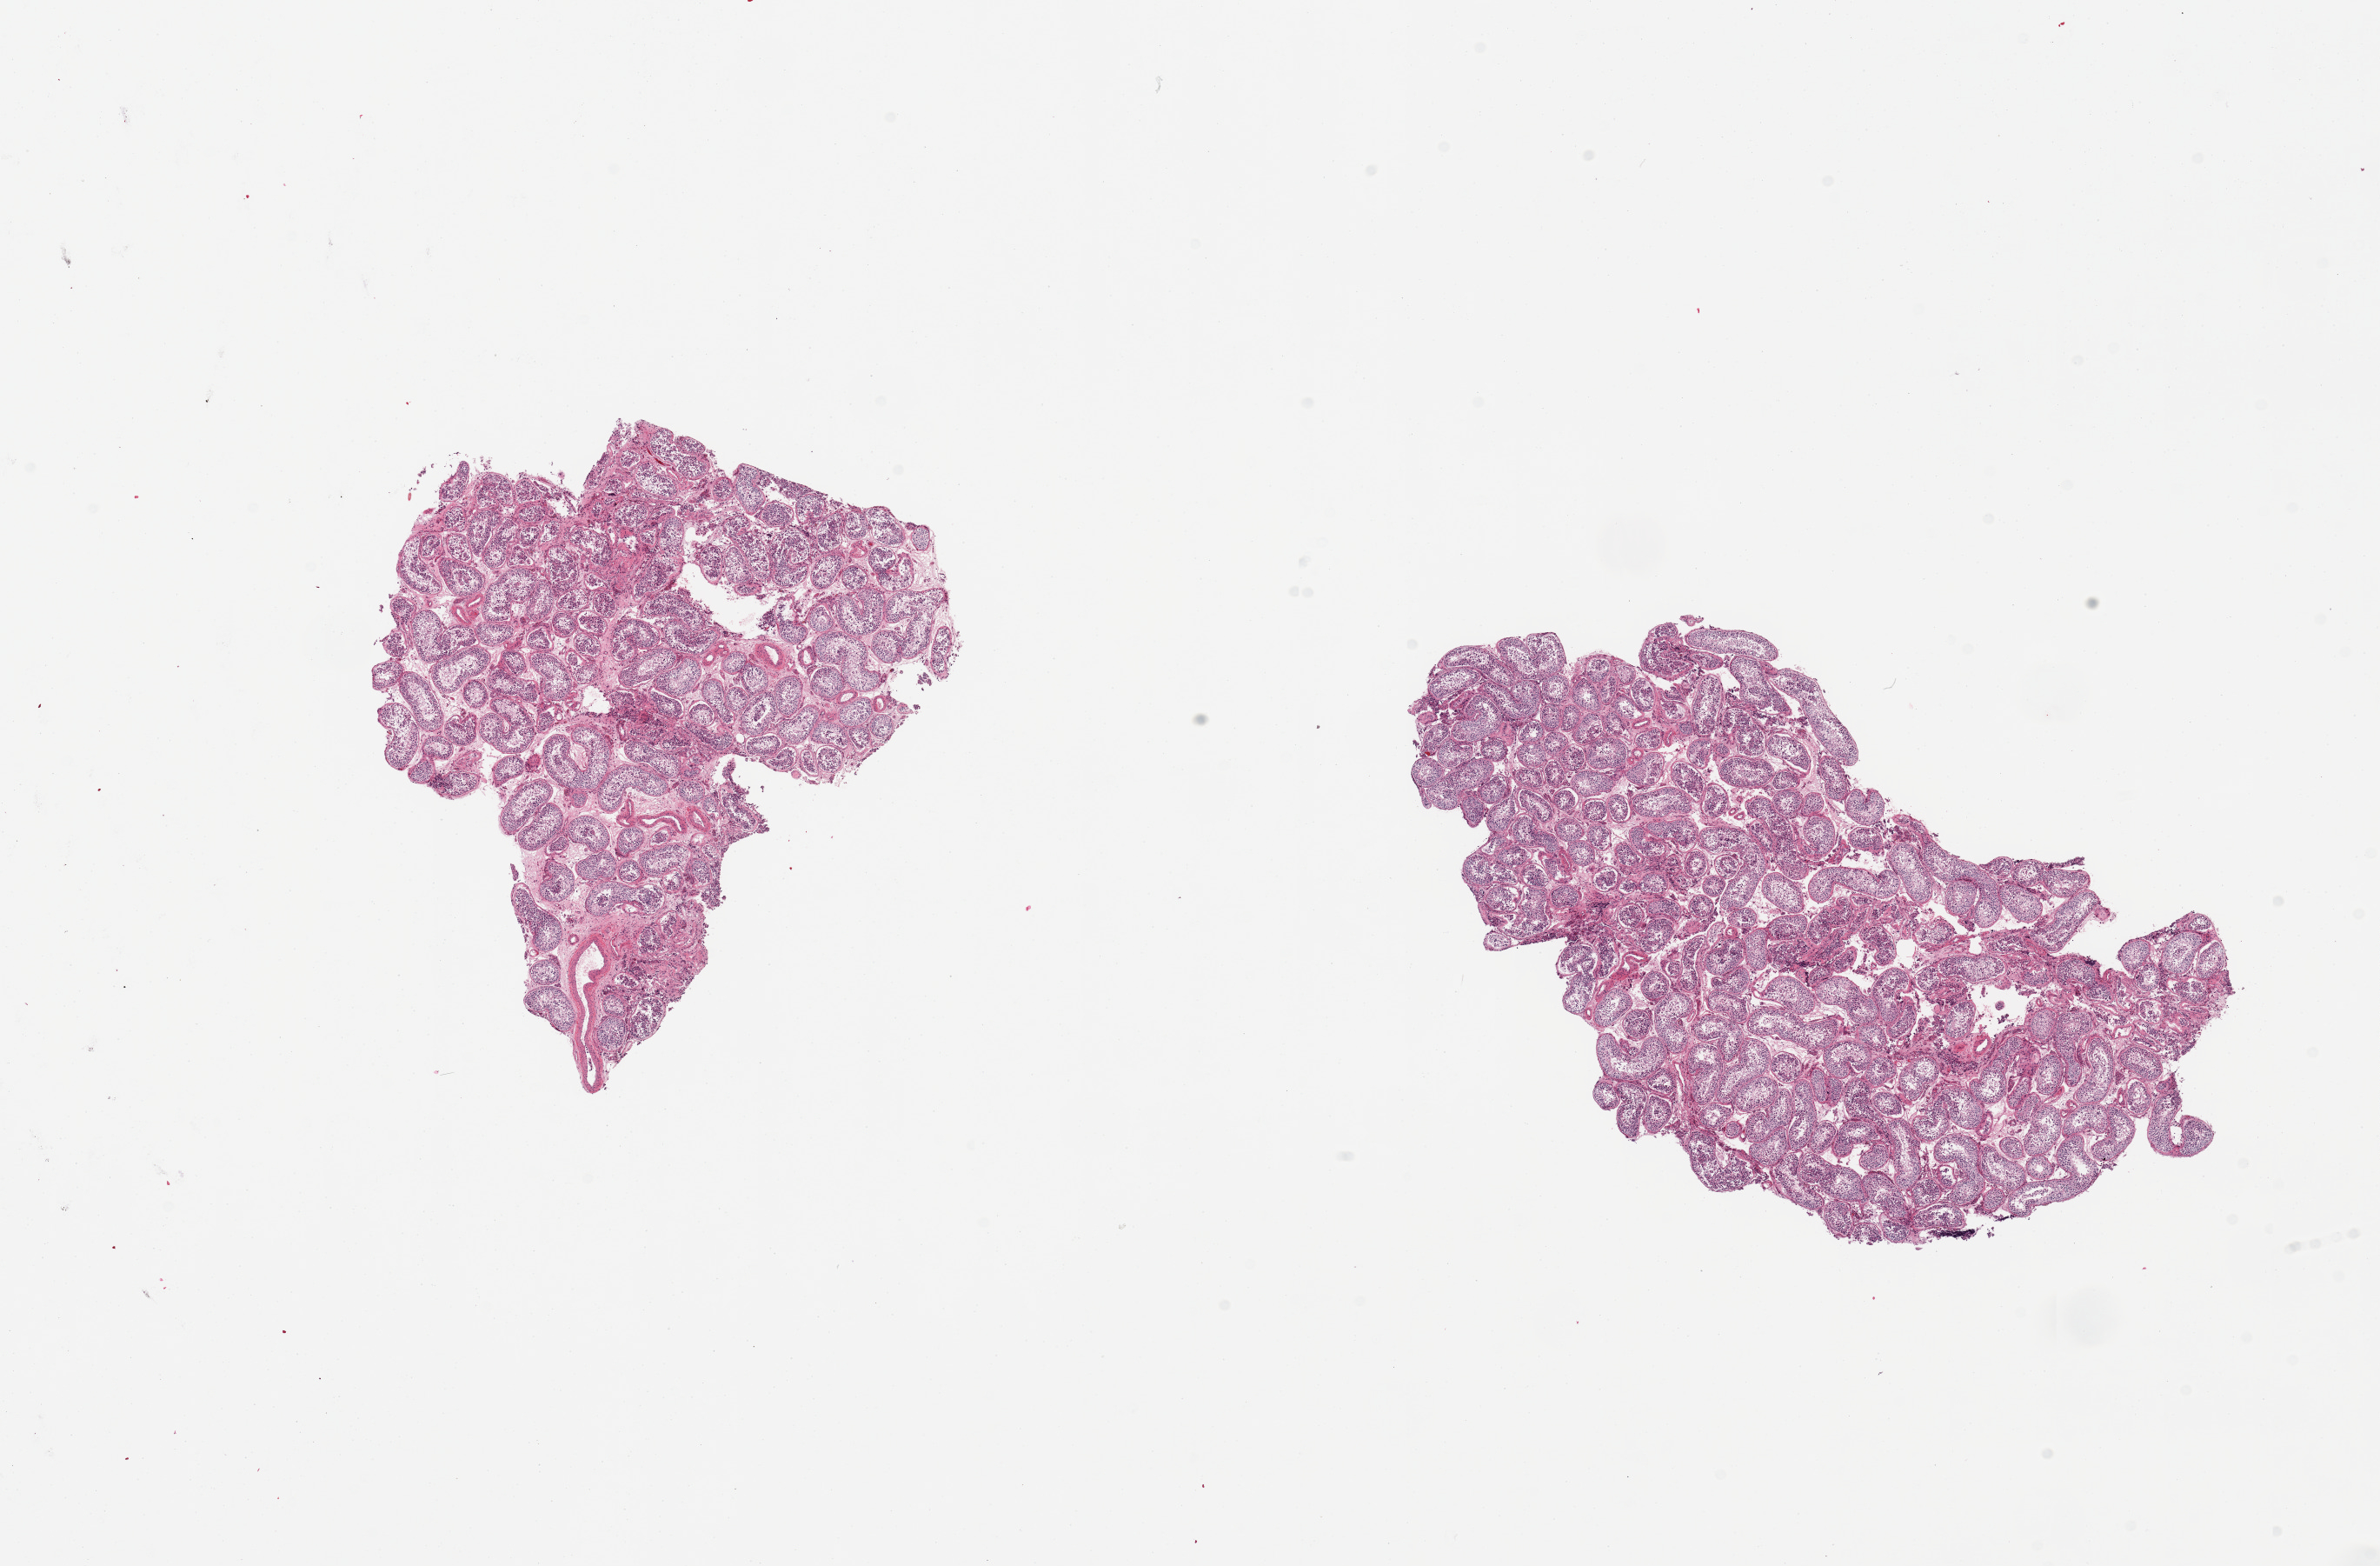
H&E whole-slide image, shown as a low-resolution overview of the whole scanned area (about 21.7 x 14.2 mm, acquisition: 20x scan); PAXgene-fixed paraffin-embedded (PFPE) section; sampled site (target tissue): testis; donor tissue sample. Male donor.
Review note (as recorded): 2 pieces, spermatogenesis is present.